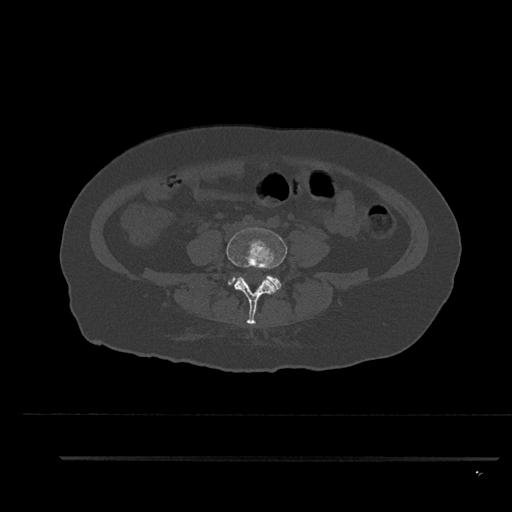
CT including the spine, one axial slice. Slice 3 of 797 in the series (ordered by position). Reconstruction kernel Br40s/3. Bone window (W 1800 / L 400 HU). 0.5 mm slice thickness. 512 × 512 image matrix, field of view 408 × 408 mm. Female patient, age 44 years. Case-level facts recorded for this patient, not image findings: primary cancer: renal; vertebrae with lytic lesions (as recorded): L1.
Structures marked on this image (semi-automatic segmentation, software-assisted and operator-edited):
- L4 vertebra: bounding box <226,228,287,325> (left, top, right, bottom; pixels)